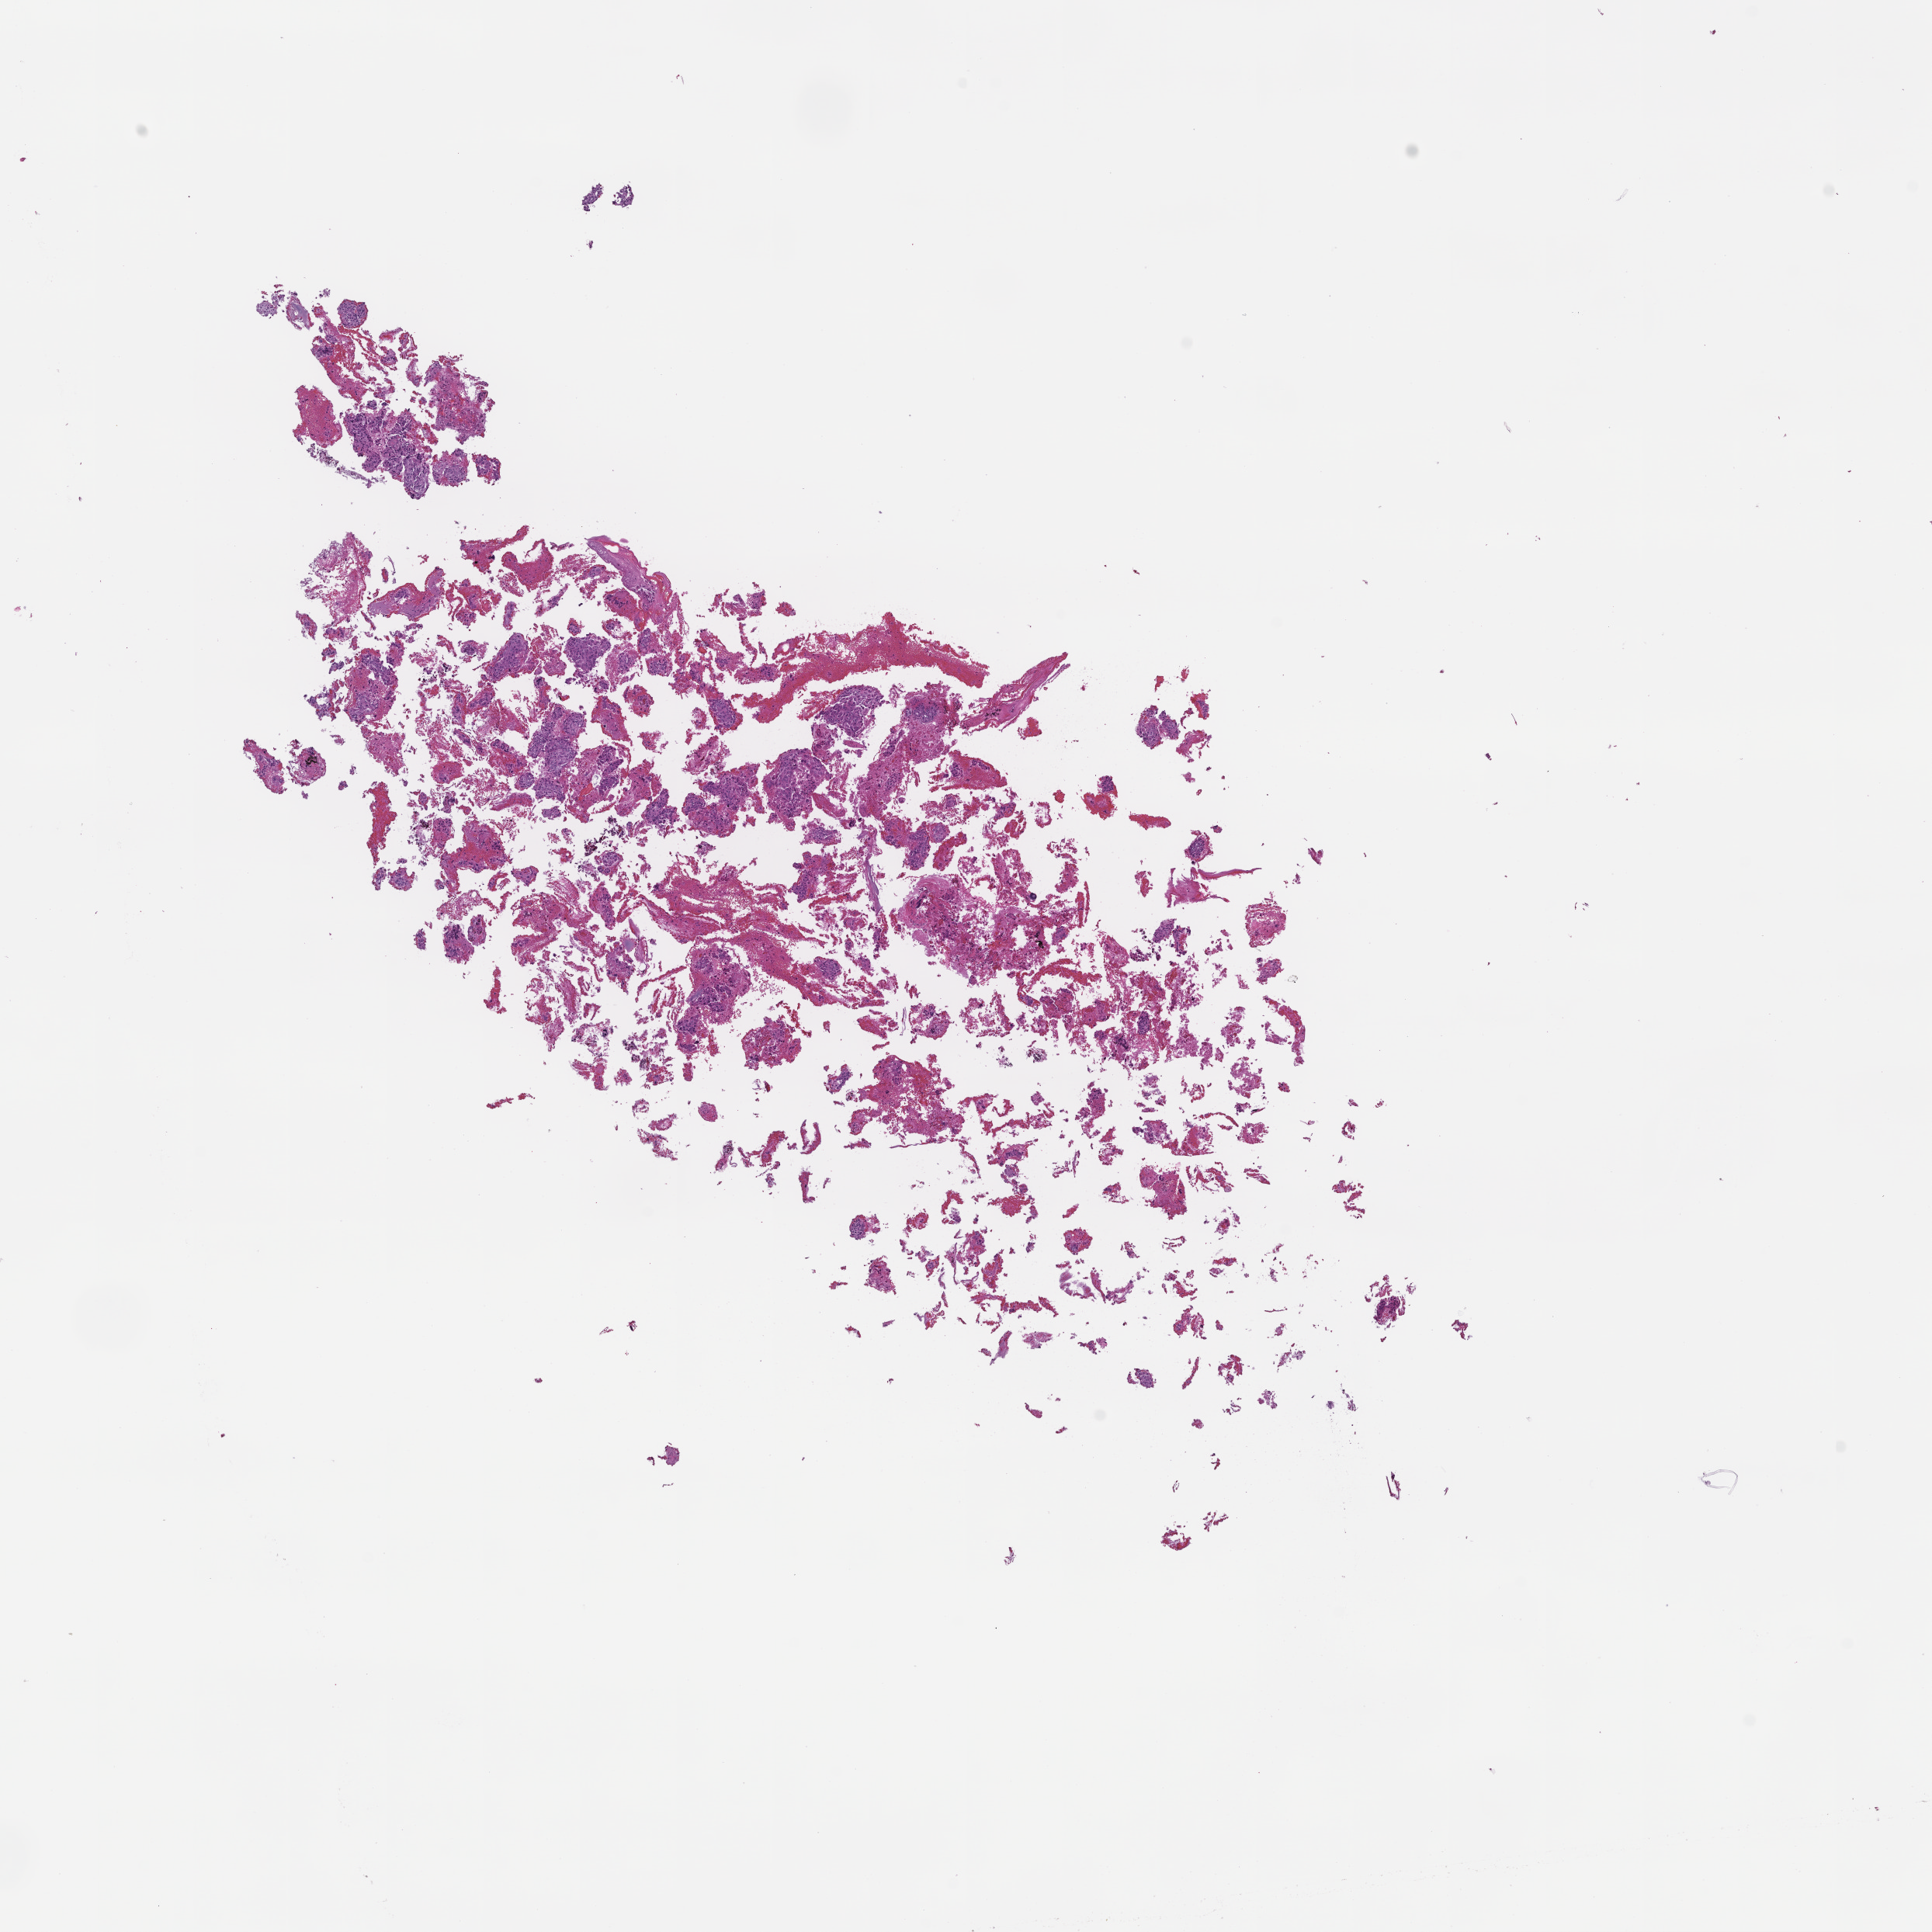
Digitized haematoxylin and eosin-stained section, a low-resolution overview of the entire scanned area, about 10.1 x 10.1 mm; formalin-fixed paraffin-embedded section. Patient: female.
* this section: metastasis (sampled organ not recorded)
* primary diagnosis of the patient: Non-Small Cell Lung Carcinoma